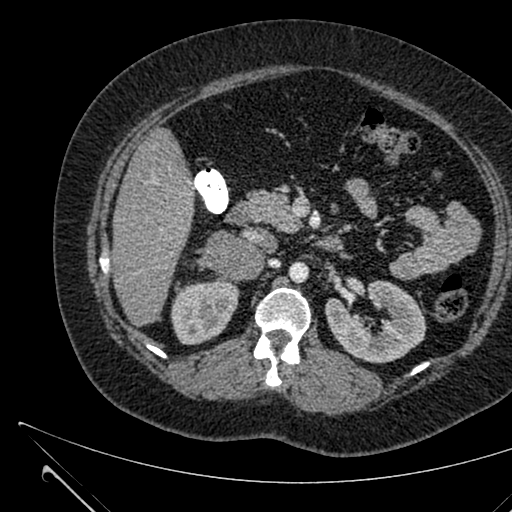
Contrast-enhanced abdominal CT, one axial slice; slice 361 of 731 in the series (ordered by position); 120 kVp; intravenous contrast given; soft-tissue window (W 400 / L 40 HU); 512 × 512 image matrix. Female patient, age 36 years. Case-level facts recorded for this patient, not image findings: diagnosis: adrenocortical carcinoma; tumour side: right adrenal; tumour size at pathology: 10 cm; Ki-67 index: 20 %.
Outlined on this slice (semi-automatic segmentation, software-assisted and operator-edited):
- mass: box from (x=206, y=232) to (x=263, y=279) px